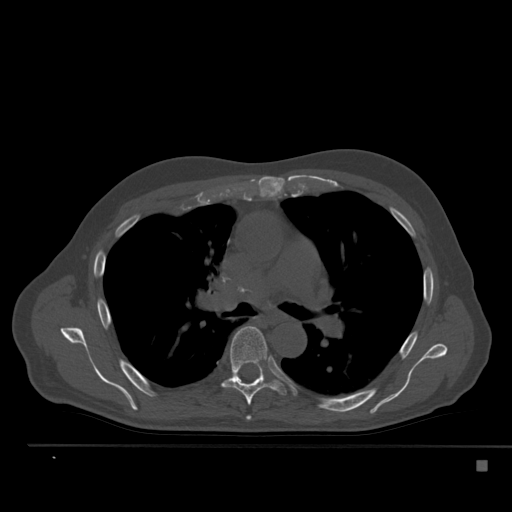
CT including the spine, one axial slice. Reconstruction kernel Br40s. 120 kVp. Bone window (W 1800 / L 400 HU). 1.5 mm slice thickness. 512 × 512 image matrix. Patient: male, 70 years. Case-level facts recorded for this patient, not image findings: primary cancer: renal; vertebrae with lytic lesions (as recorded): T4, T6, T10, T12, L3, L4, L5.
Outlined on this slice (semi-automatic segmentation, software-assisted and operator-edited):
- T5 vertebra: box from (x=246, y=416) to (x=251, y=420) px
- T6 vertebra: (x=222, y=326)–(x=286, y=406)